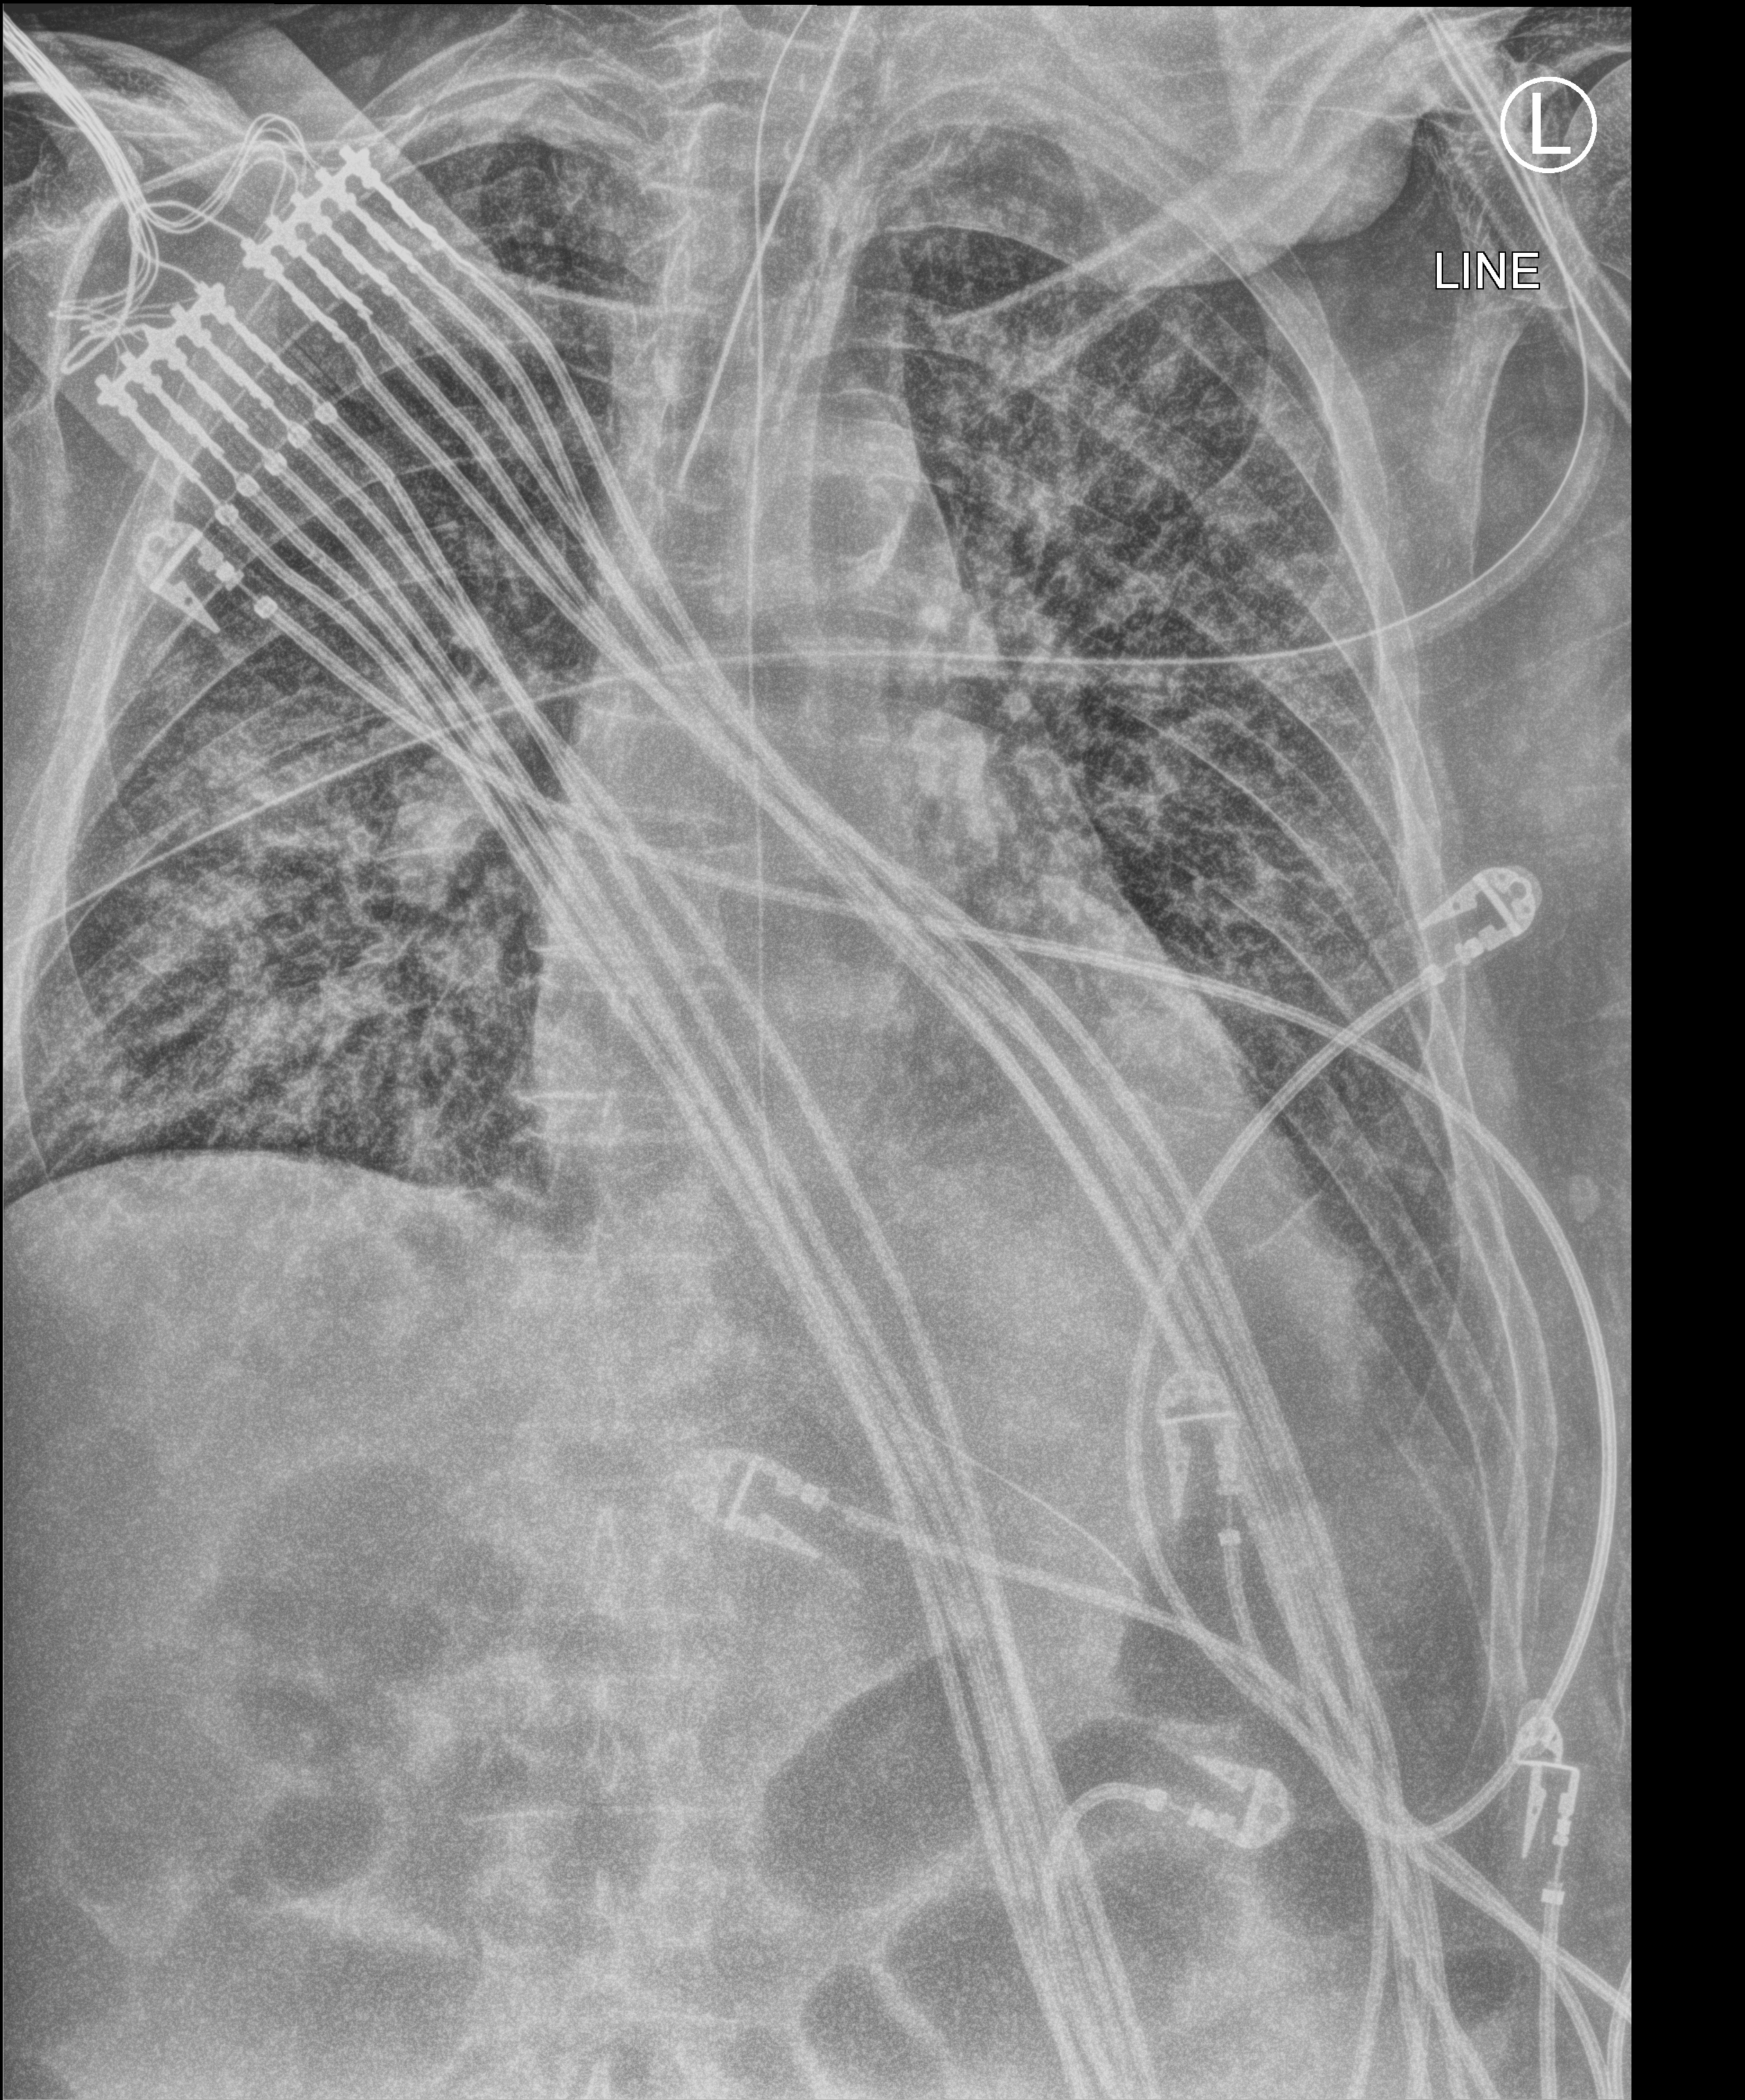
Bedside chest radiograph (computed radiography). Male patient hospitalised with COVID-19, age 60–74 years.
Hospital-stay facts (about this admission, not read from this image; timing relative to this image not recorded): length of hospital stay: 25 days; mechanically ventilated during this hospital stay: yes.